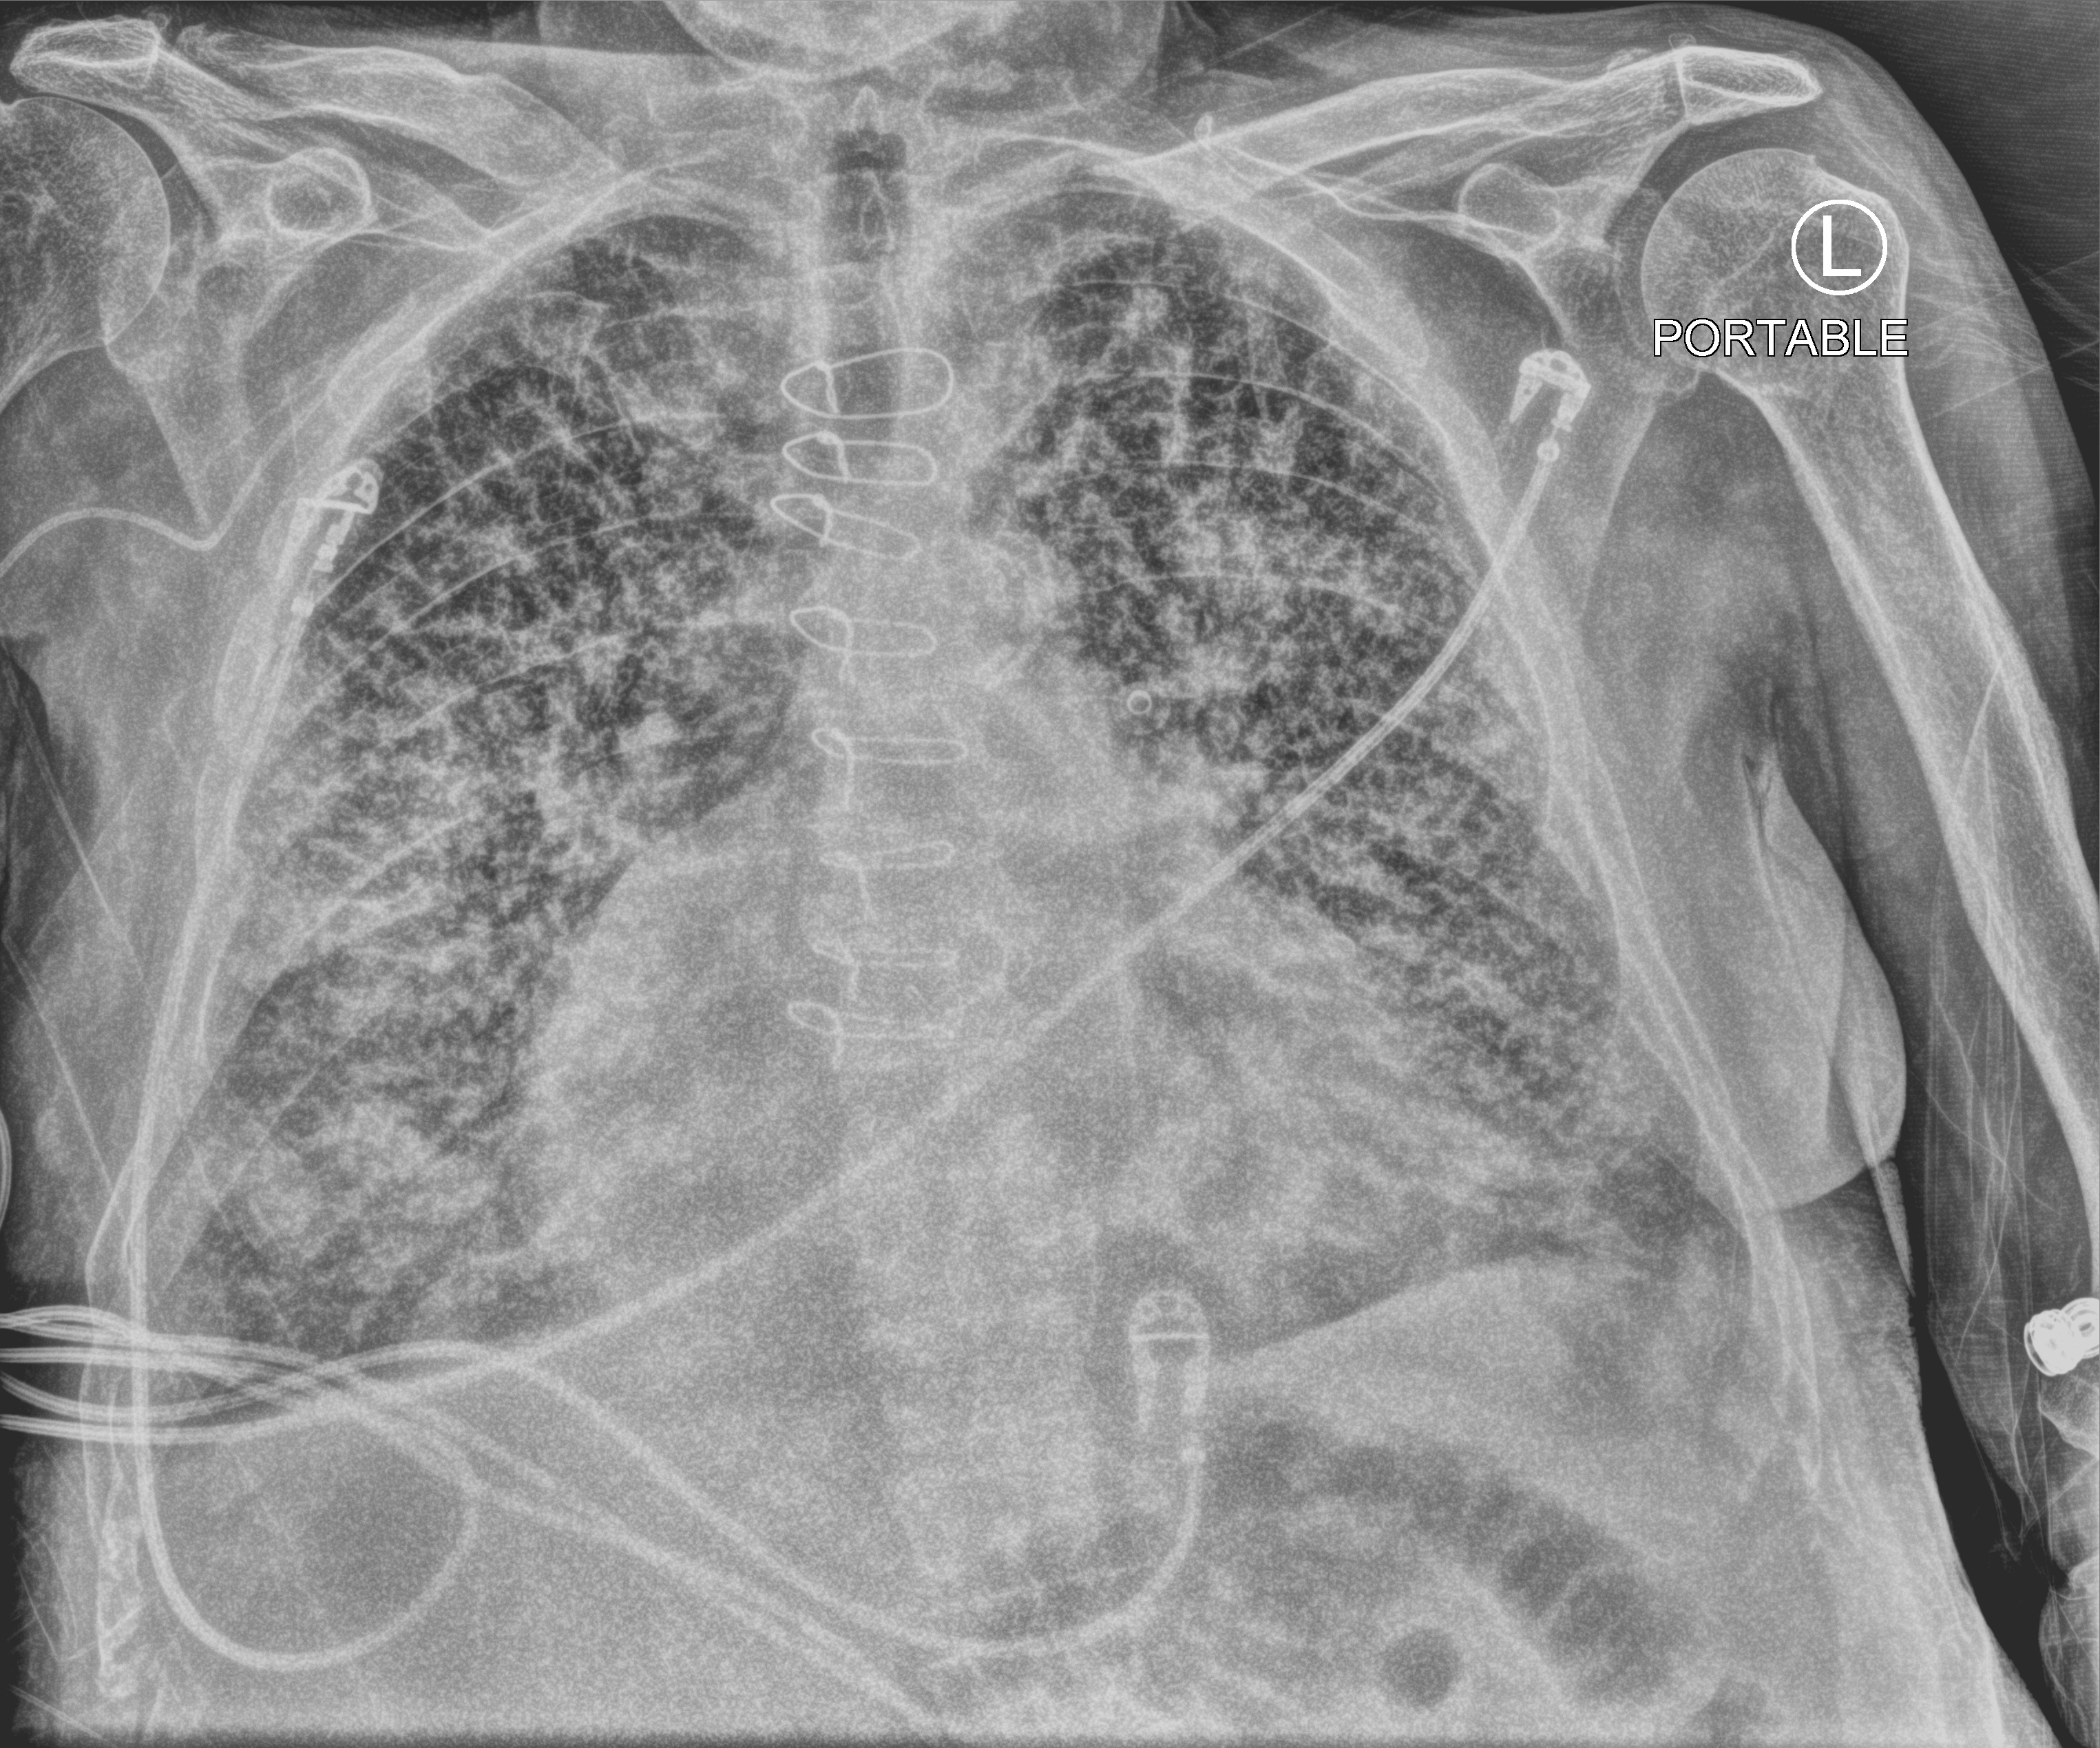
Chest X-ray (portable). Male patient hospitalised with COVID-19, age 75–90 years.
Hospital-stay facts (about this admission, not read from this image; timing relative to this image not recorded): mechanically ventilated during this hospital stay: yes; length of hospital stay: 40 days.